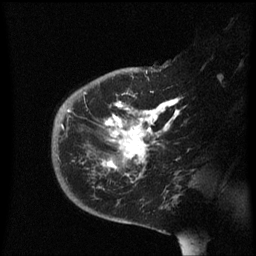
Breast MRI (dynamic contrast-enhanced), one sagittal slice. Slice 40 of 60 in the series (ordered by position). Dynamic contrast-enhanced series, image 2 of 3 at this slice position (ordered by acquisition). 1.5 T. TE 4.2 ms, TR 8.4 ms. 256 × 256 image matrix. Female patient, age 38 years. From the clinical record (not read from this slice): setting: breast cancer imaged before/during neoadjuvant chemotherapy; receptor status: HER2-positive.
Outlined on this slice (semi-automatic segmentation, software-assisted and operator-edited):
- analysis volume of interest (the breast-tissue region the enhancement analysis was run in; not a lesion): bounding box (x1, y1, x2, y2) in pixels: (52, 78, 182, 213)
- tumour enhancement mask (voxels above the 70 % enhancement threshold inside the analysis volume of interest): (61, 92, 180, 177)